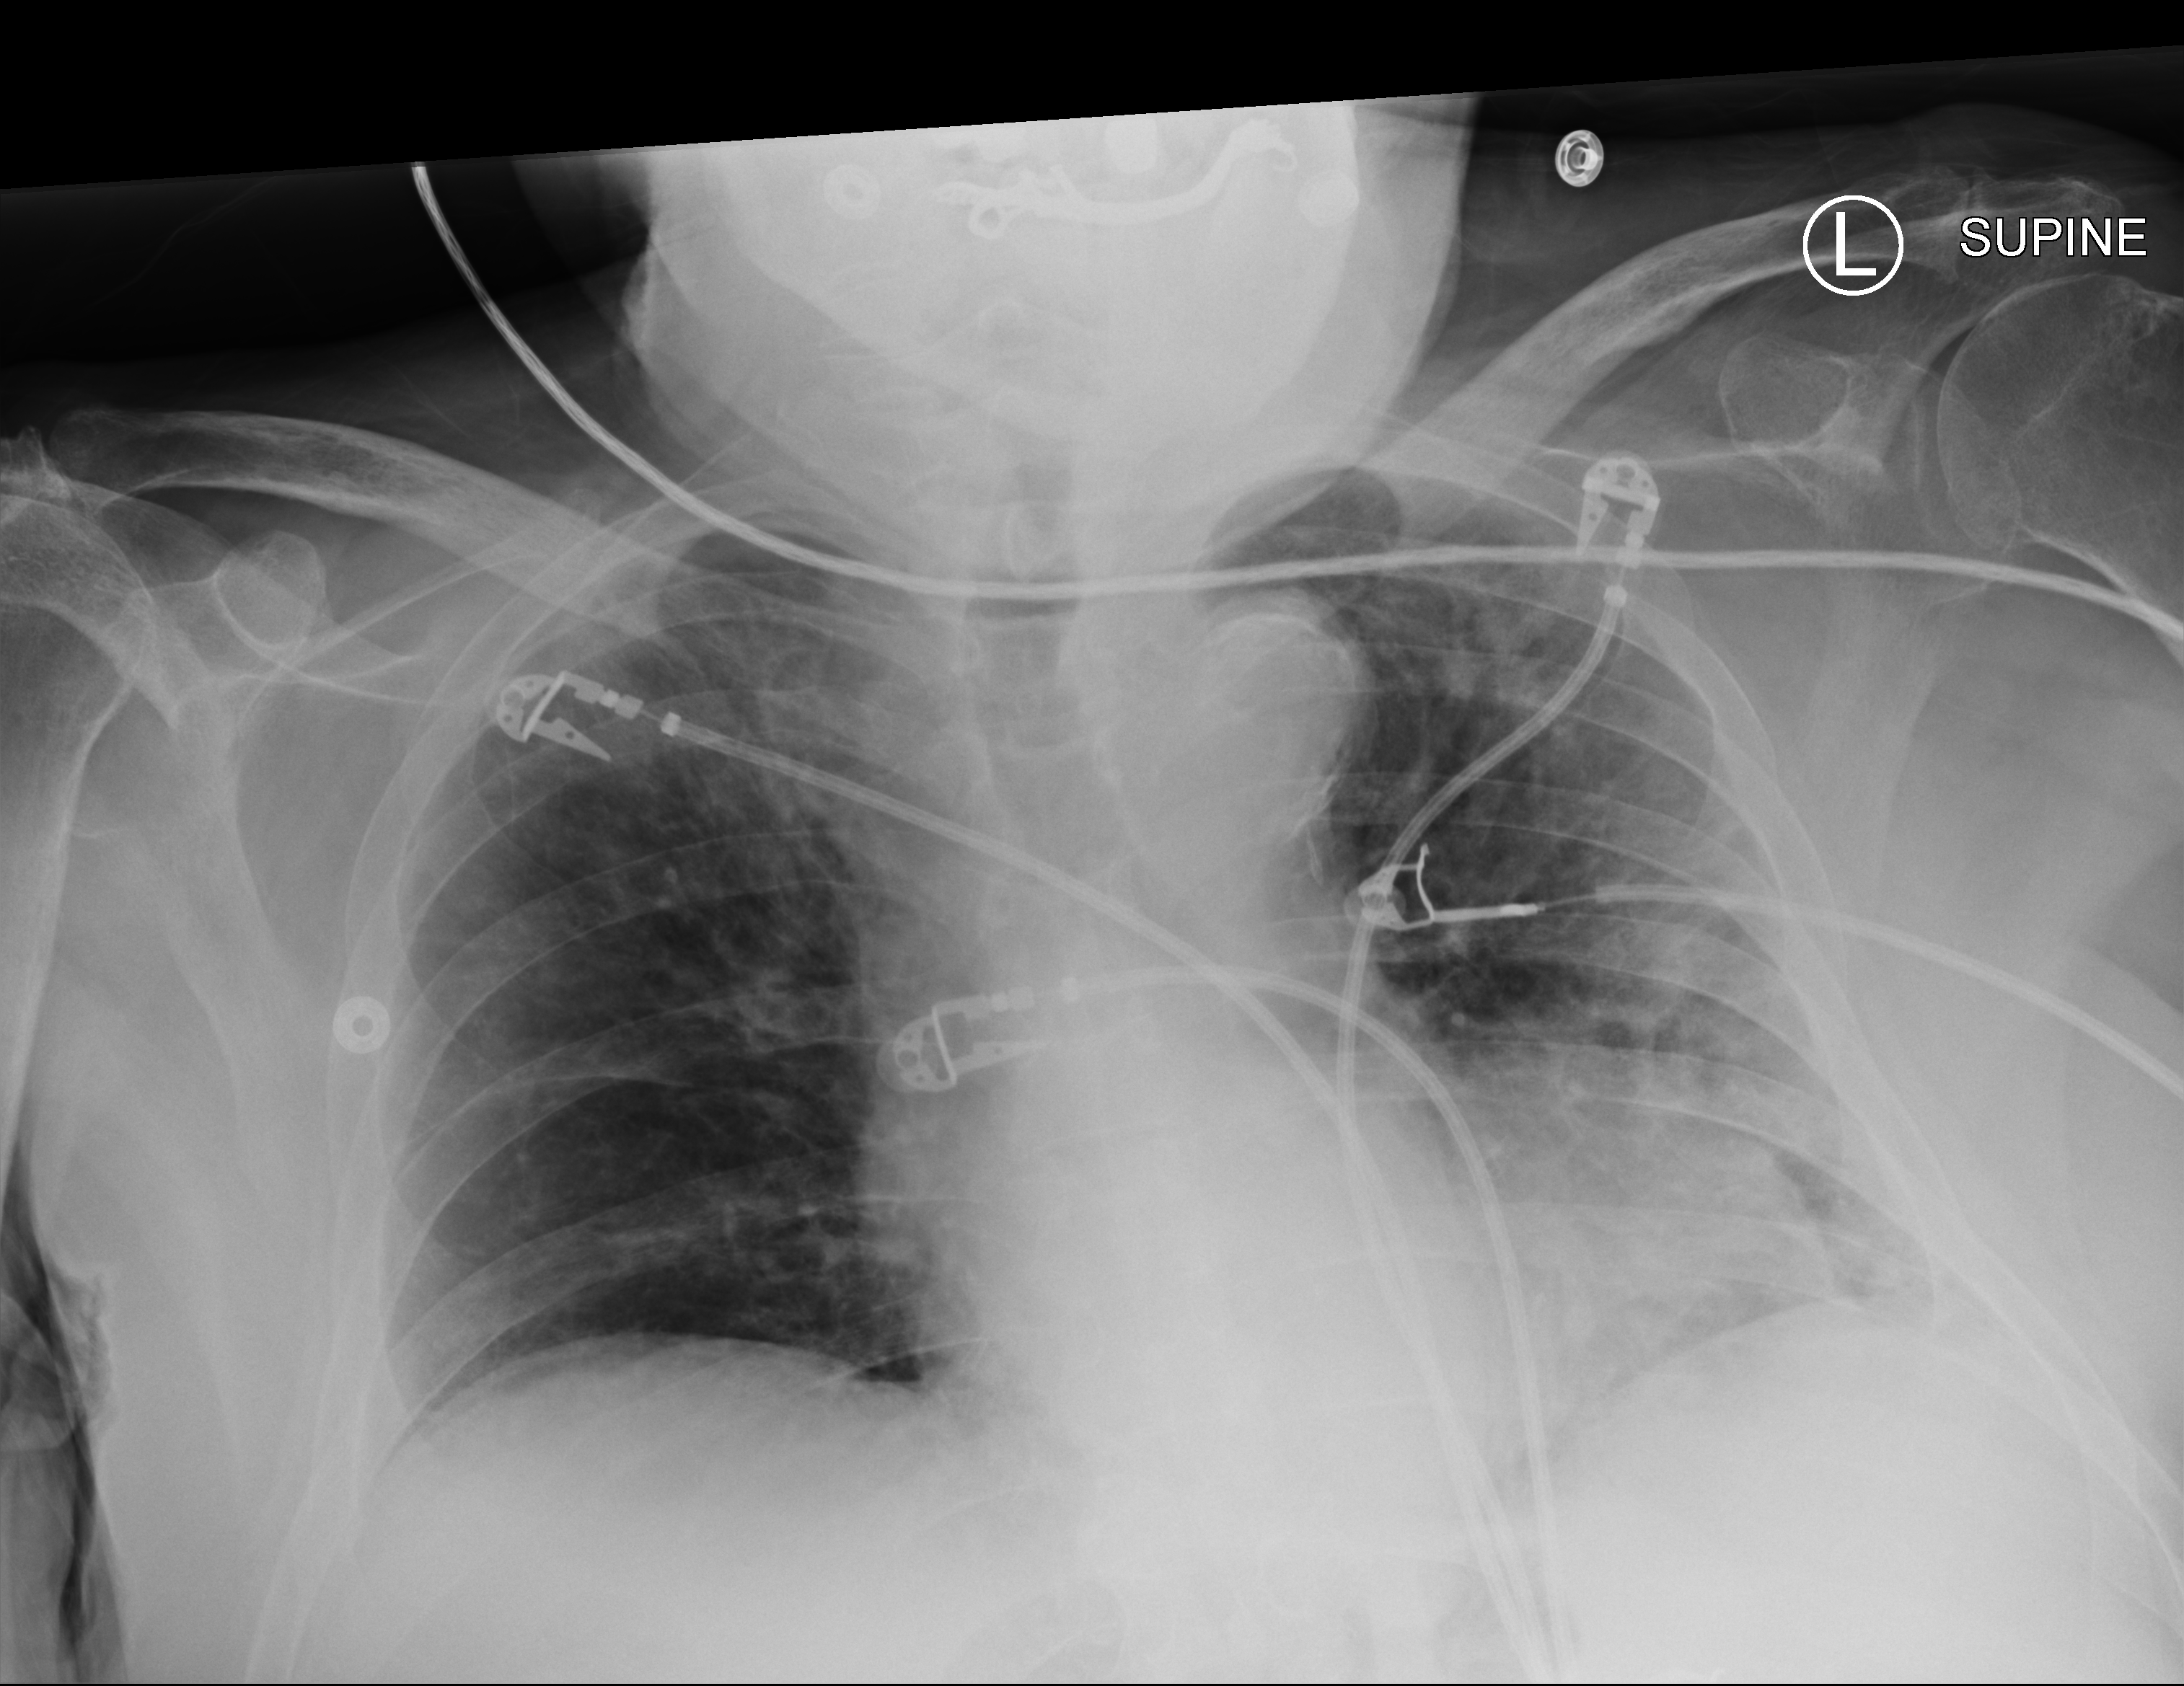
Bedside chest radiograph (computed radiography), anteroposterior (AP) projection. Patient hospitalised with COVID-19; male, aged 75–90 years.
Hospital-stay facts (about this admission, not read from this image; timing relative to this image not recorded): admitted to intensive care during this hospital stay: no; diabetes (admission record): yes.